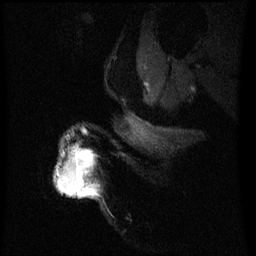
Breast MRI (dynamic contrast-enhanced), one sagittal slice; dynamic contrast-enhanced series, image 2 of 3 at this slice position (ordered by acquisition); 1.5 T; TE 4.2 ms, TR 8 ms; 2.2 mm slice thickness; 256 × 256 image matrix, field of view 200 × 200 mm. Patient: female, 50 years.
Annotated regions visible in this slice (semi-automatic segmentation, software-assisted and operator-edited):
- analysis volume of interest (the breast-tissue region the enhancement analysis was run in; not a lesion): box from (x=58, y=150) to (x=89, y=195) px
- tumour enhancement mask (voxels above the 70 % enhancement threshold inside the analysis volume of interest): (x=58, y=152)–(x=89, y=195)